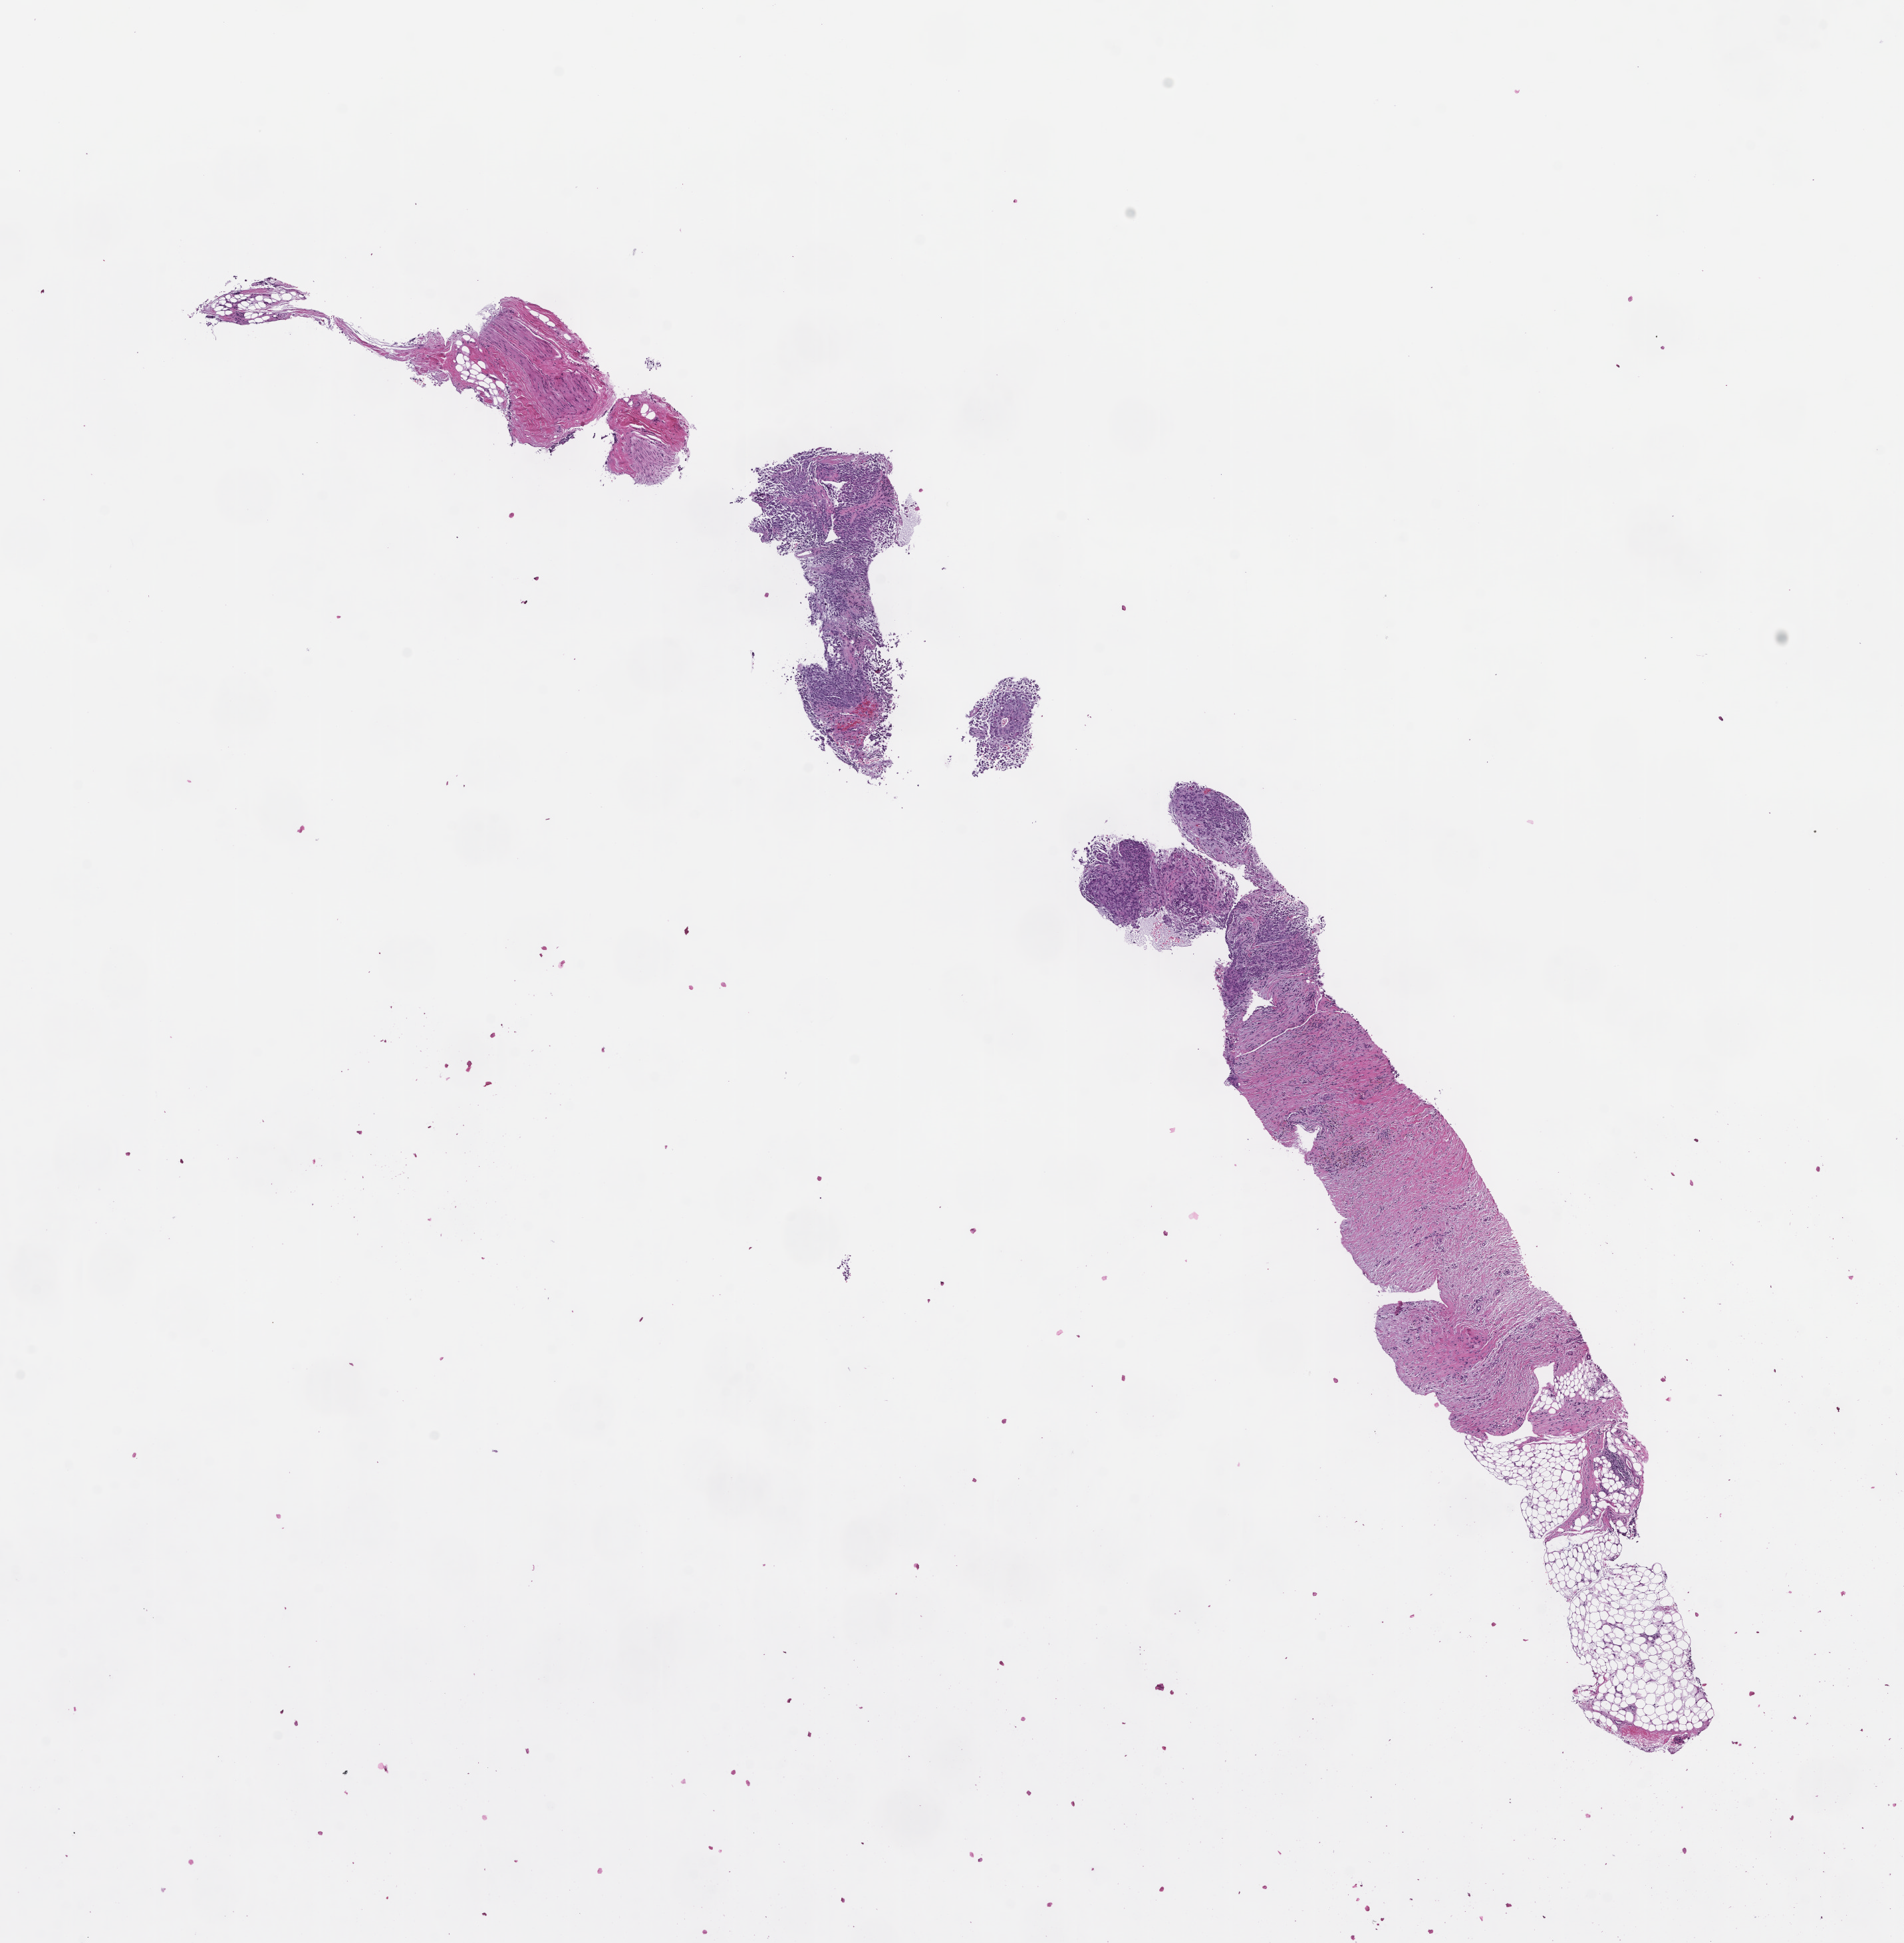
Whole-slide image, H&E stain — low-resolution overview of the scanned area, about 11.6 x 11.8 mm. Formalin-fixed, paraffin-embedded (FFPE) tissue. Specimen time point: collected at baseline (before treatment). Patient sex: male.
- this section: metastatic tumor tissue
- patient diagnosis (primary): Small Cell Lung Carcinoma